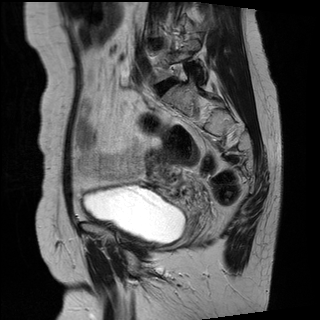
Pelvic MRI for cervical cancer, one sagittal slice. Position 18 of 27 along the scan axis. T2-weighted. 1.5 T. TE 89 ms, TR 2740 ms. 4 mm slice thickness. 320 × 320 image matrix, field of view 260 × 260 mm. Female patient, age 42 years.
Outlined on this slice (manually delineated by an expert):
- uterus and cervix: bounding box [x1, y1, x2, y2] px = [145, 148, 170, 167]